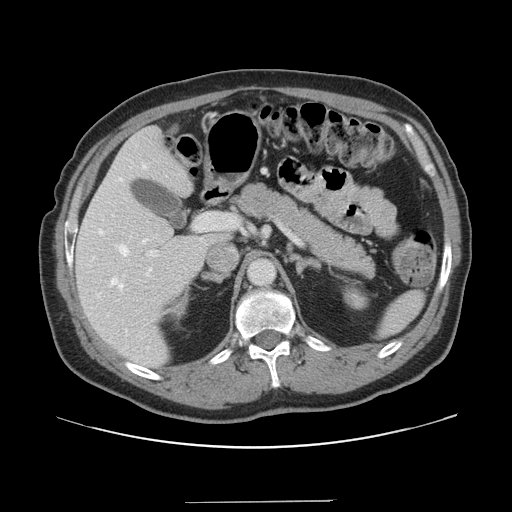
Contrast-enhanced abdominal CT, one axial slice; slice 88 of 151 in the series (ordered by position); 120 kVp; intravenous contrast given; soft-tissue window (W 400 / L 40 HU); 512 × 512 image matrix, field of view 399 × 399 mm. Male patient, age 63 years. From the clinical record (not read from this slice): diagnosis: colorectal cancer liver metastases, imaged before liver resection; multiple liver metastases: no; largest metastasis: 2.1 cm; disease in both lobes: no.
Outlined on this slice (expert manual segmentation):
- hepatic veins: box from (x=99, y=164) to (x=151, y=335) px
- liver: (x=76, y=128)–(x=225, y=368)
- planned liver remnant (the part of the liver to remain after resection): (x=76, y=129)–(x=224, y=368)
- portal vein (with intrahepatic branches): (x=147, y=213)–(x=237, y=257)